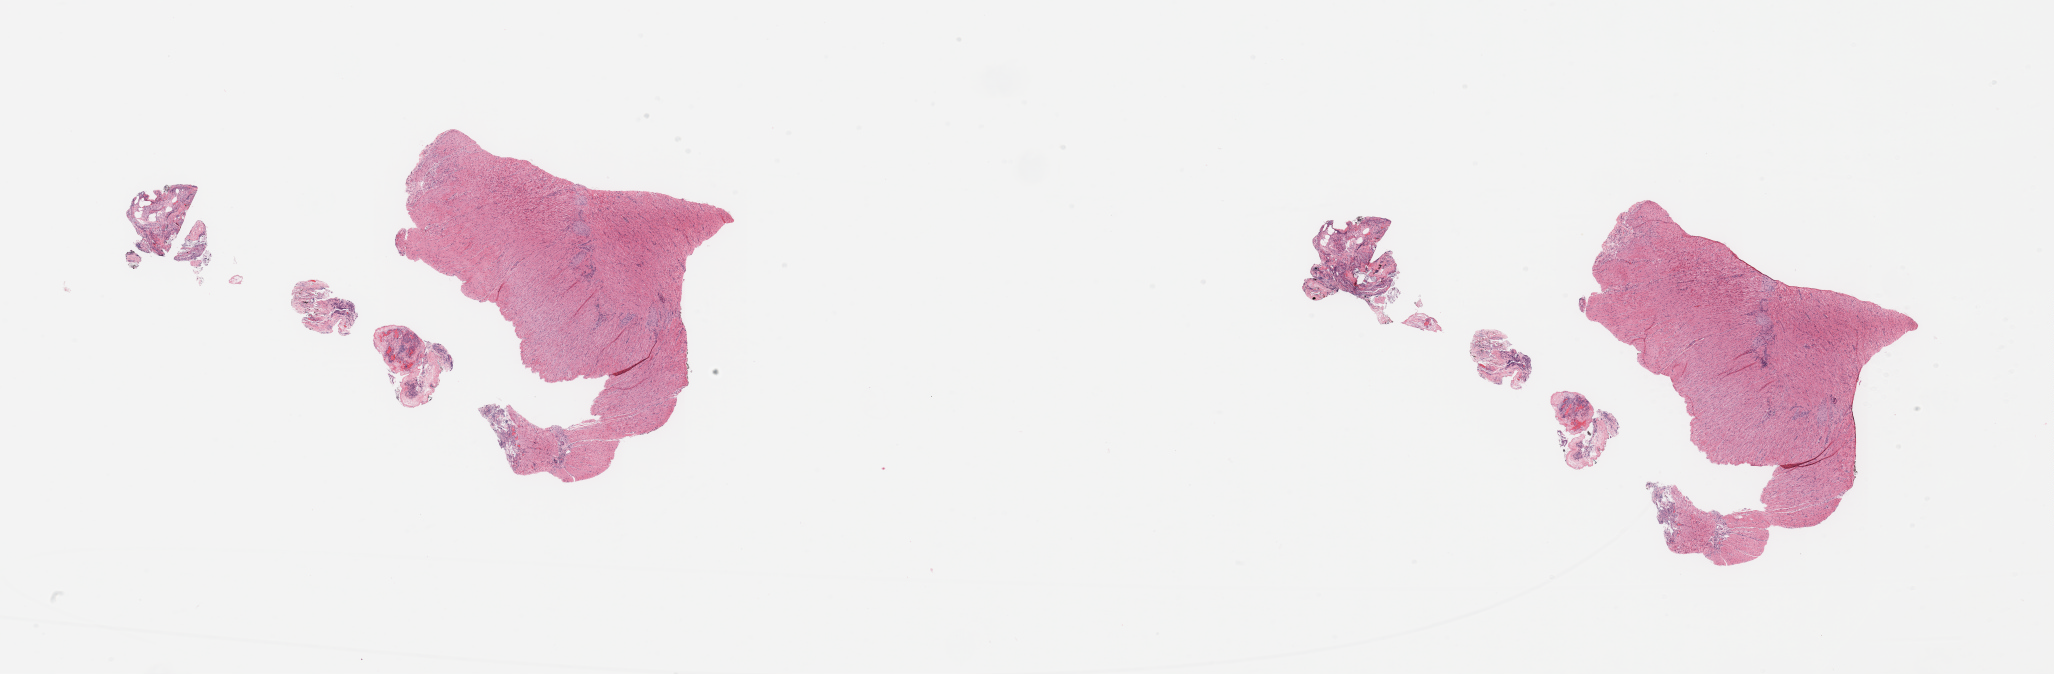
Whole-slide histology image, Hematoxylin and eosin (H&E) stained, low-resolution overview of the scanned area, about 32.5 x 10.7 mm (from a 20x scan); tumour tissue sample, sampled site: pancreas. Male, 66 y/o. Histologic grade: G3 (poorly differentiated). Slide review estimates, as recorded: tumour nuclei 1%, necrosis 0%.
* primary tumour site (as recorded): head
* histologic diagnosis: Infiltrating duct carcinoma, NOS
* AJCC pathologic stage: IIB